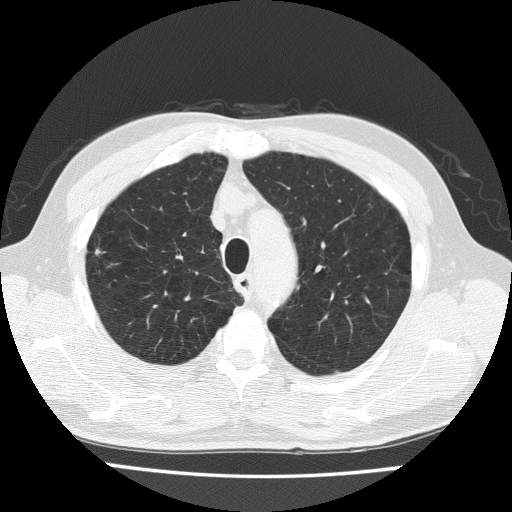
Chest CT (low-dose screening protocol), one axial image, first (baseline) screen, lung window (W 1500 / L -600 HU), lung (sharp) reconstruction kernel (FC51), slice 38 of 205 in the series, 512 × 512 image matrix, field of view 350 × 350 mm. Male, age 73 years at enrolment.
Lesion marked by an expert reader, bounding box [x1, y1, x2, y2] px = [80, 237, 114, 269]. Reader record for this screening exam (exam-level; its link to the box is not recorded): non-calcified nodule or mass ≥4 mm, right upper lobe, 4 × 4 mm, spiculated (stellate) margins, soft tissue attenuation. Later outcome: lung cancer diagnosed 170 days after this screen — adenocarcinoma, NOS, right upper lobe, poorly differentiated (G3), stage IA (AJCC 6th edition), 60 mm at pathology.